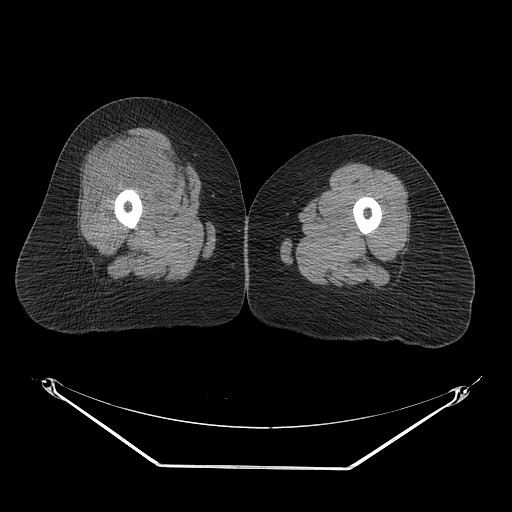
CT of an extremity soft-tissue mass (from a PET/CT study), one axial slice. Position 27 of 267 along the scan axis. Reconstruction kernel STANDARD. 140 kVp. Soft-tissue window (W 400 / L 40 HU). 3.75 mm slice thickness. 512 × 512 image matrix. Female patient. Case-level facts recorded for this patient, not image findings: histological type: malignant solitary fibrous tumor; grade: intermediate; site of the primary tumour: right thigh.
Structures marked on this image (expert contour drawn on MRI and transferred to this co-registered scan by the dataset authors):
- gross tumour volume including surrounding oedema: bounding box <100,130,202,211> (left, top, right, bottom; pixels)
- gross tumour volume (mass): <103,135,193,202>